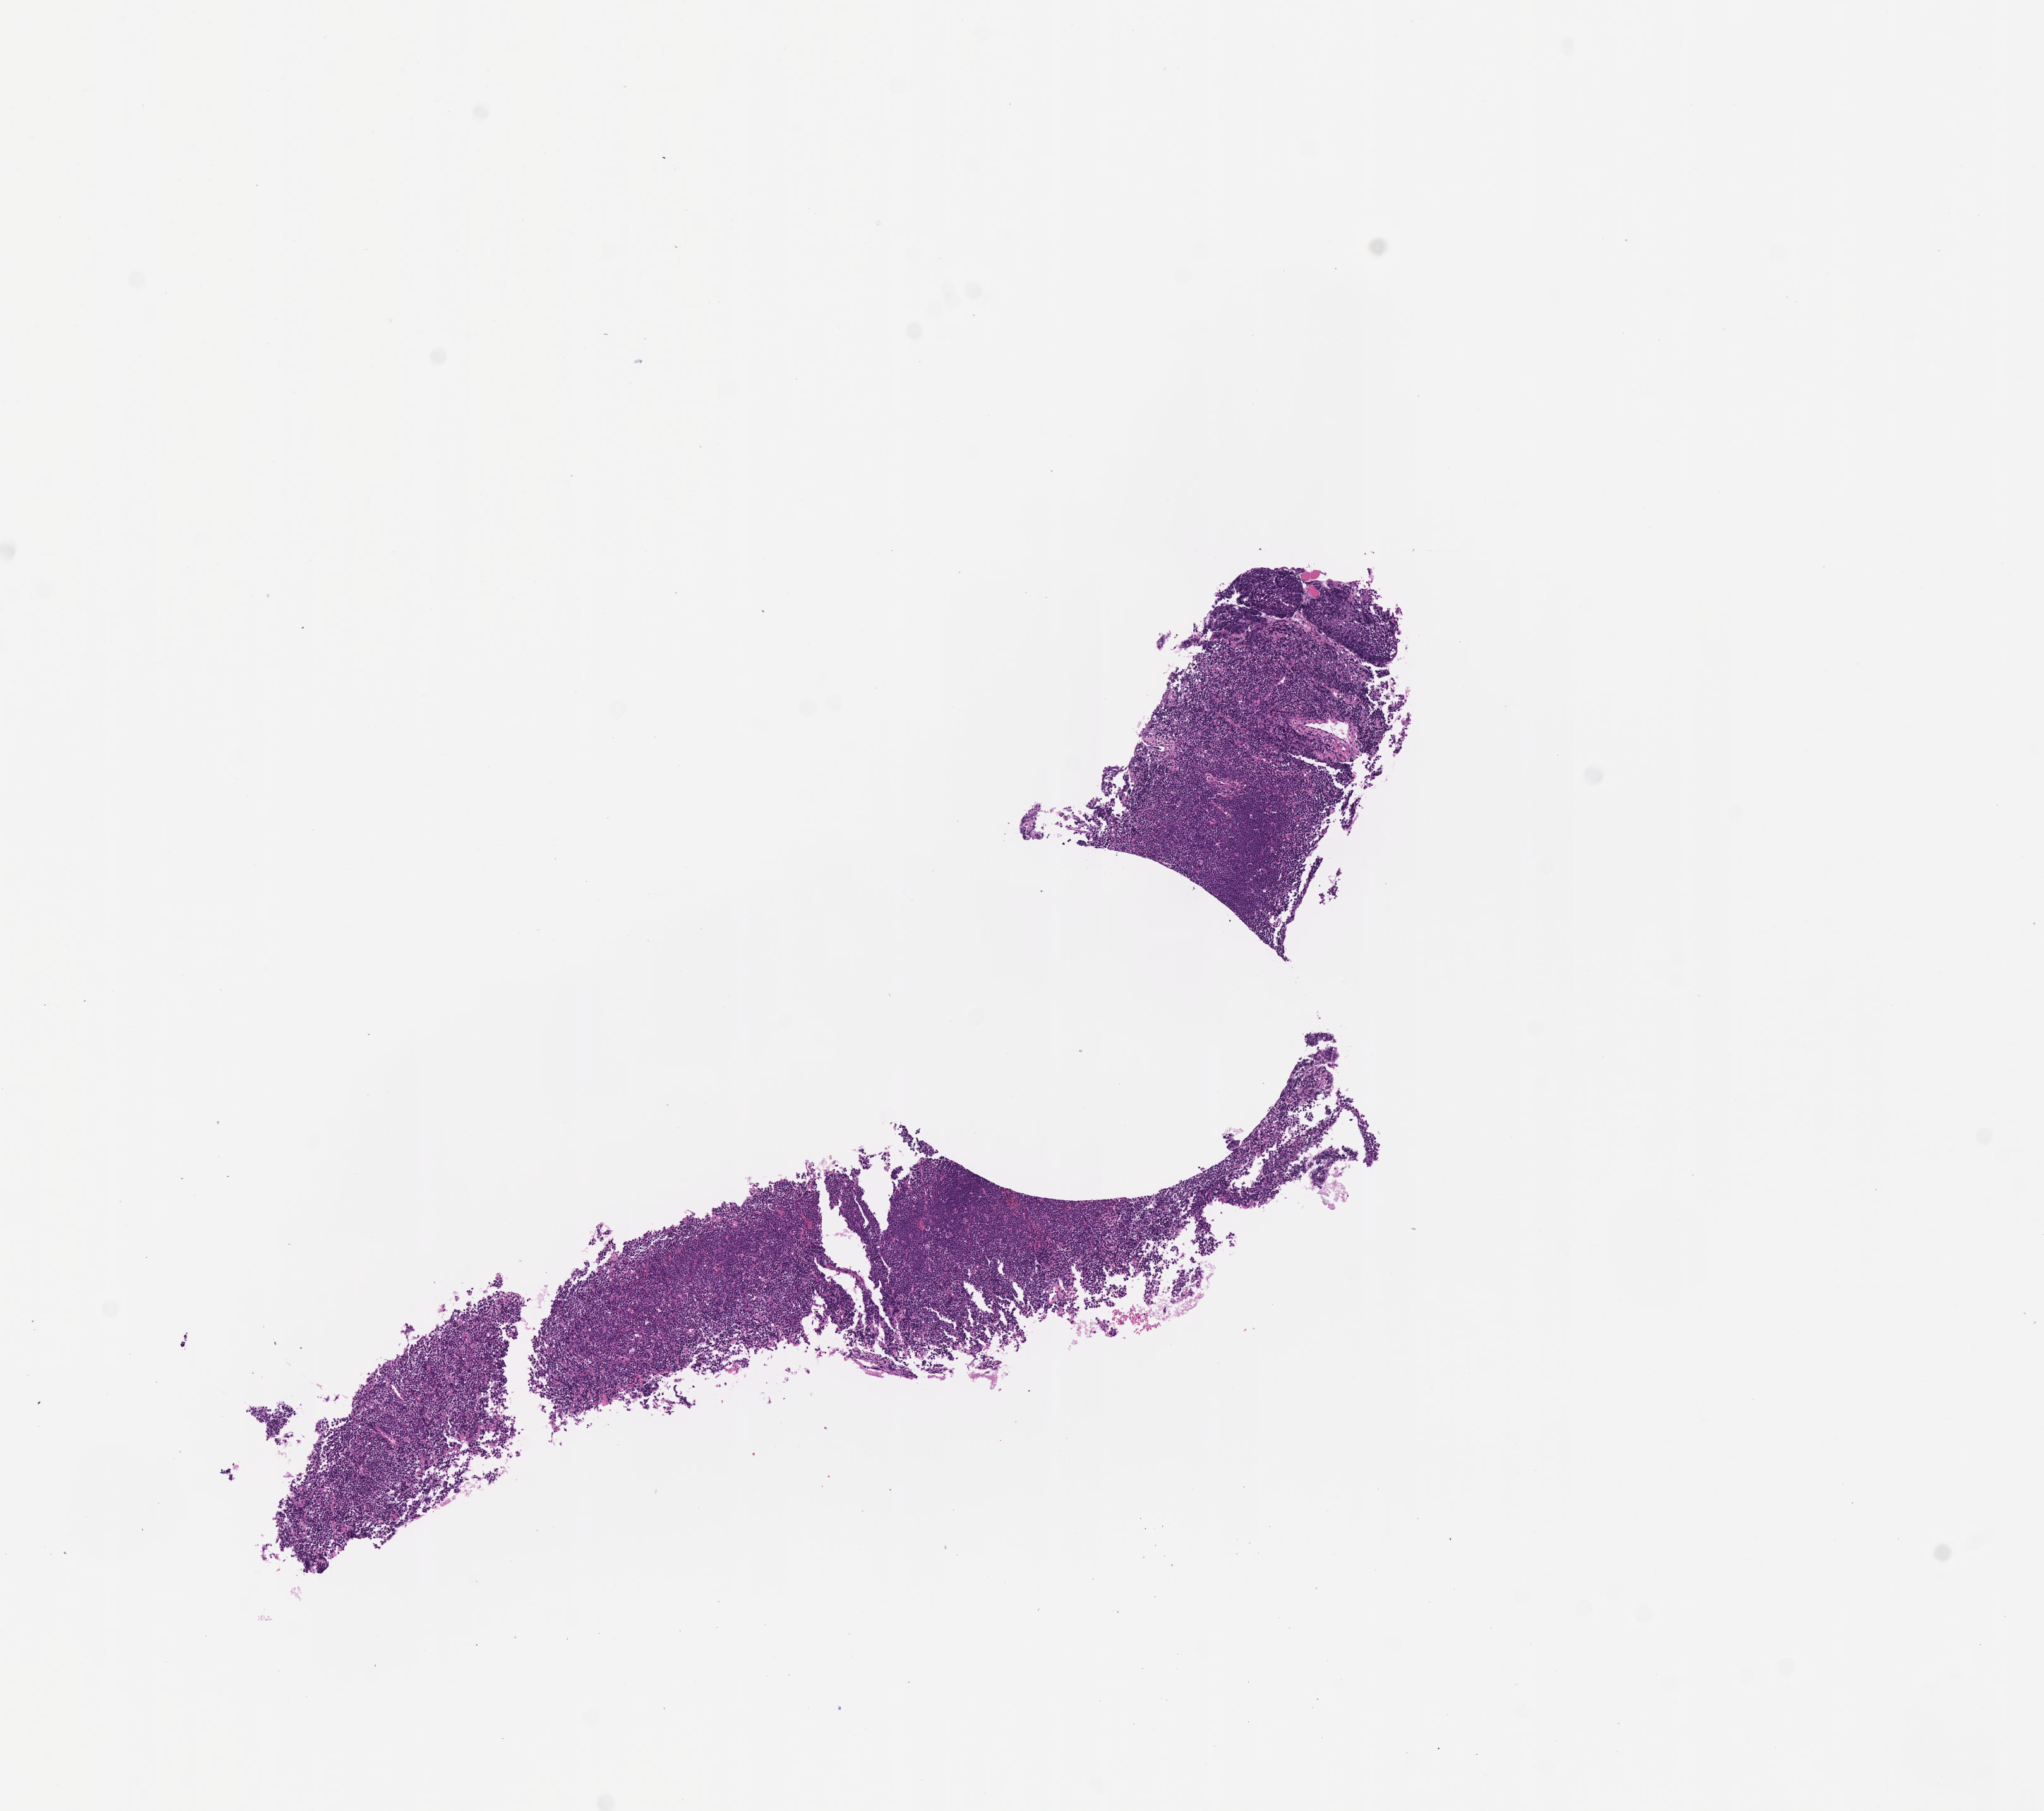
Hematoxylin and eosin (H&E) whole-slide image — low-resolution overview of the scanned area, about 6.5 x 5.8 mm; tumor tissue; anatomic site: cranium. Patient: male, age at initial diagnosis 6 years.
Histologic diagnosis: Burkitt lymphoma, NOS.